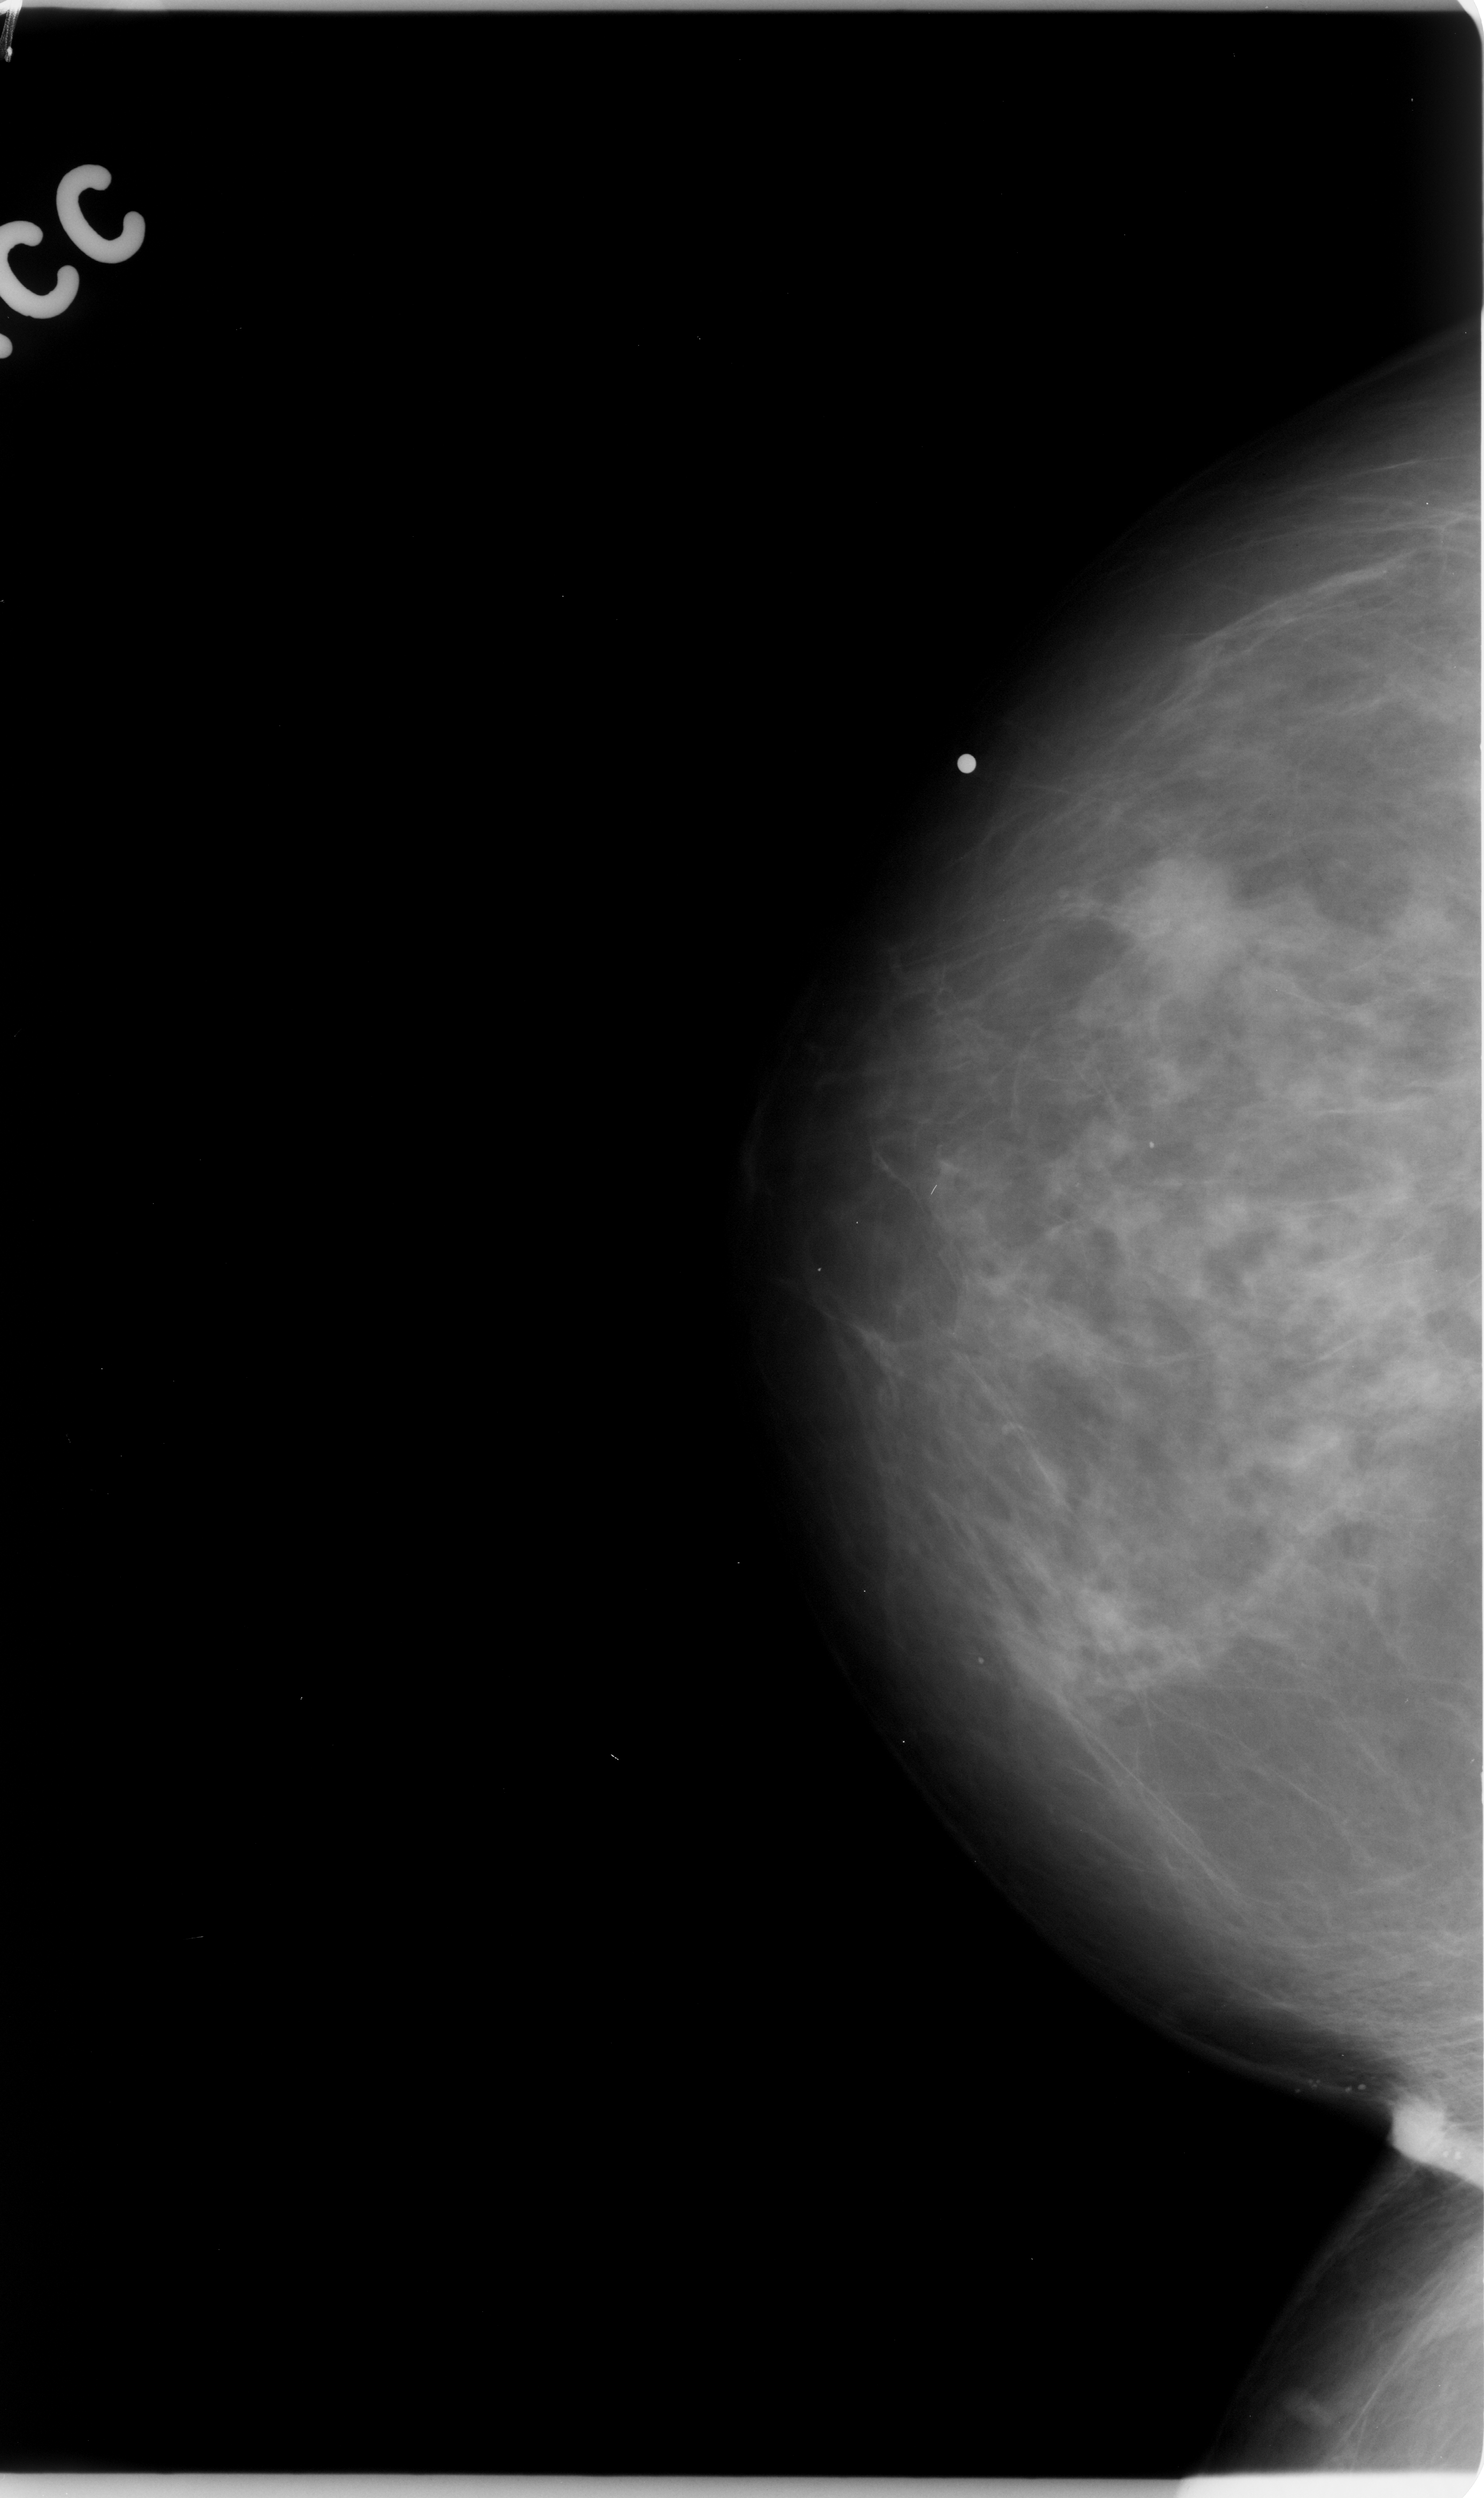
Digitized screen-film mammogram; right breast; CC view.
Abnormality record for this image: mass, shape irregular, margins microlobulated; BI-RADS assessment category 5; pathology (as recorded): malignant.